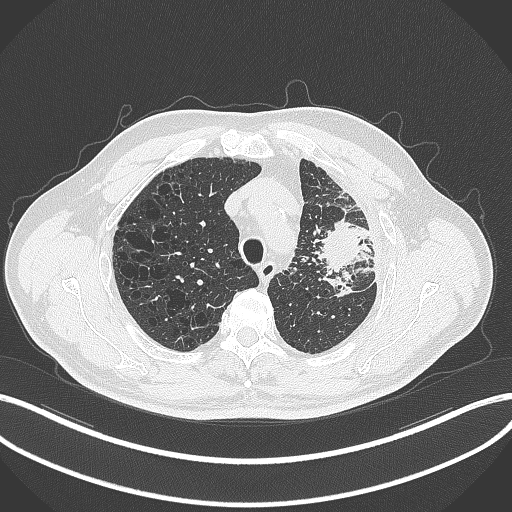
Chest CT, one axial slice; position 252 of 297 along the scan axis; reconstruction kernel B70f; lung window (W 1500 / L -600 HU); 1 mm slice thickness; 512 × 512 image matrix. Male patient, age 68 years. From the clinical record (not read from this slice): clinical TNM (as recorded): T3 N3 M1.
Annotated regions visible in this slice (rectangle marked by the reading radiologist):
- lung tumour (recorded histology: adenocarcinoma): box from (x=319, y=205) to (x=363, y=275) px